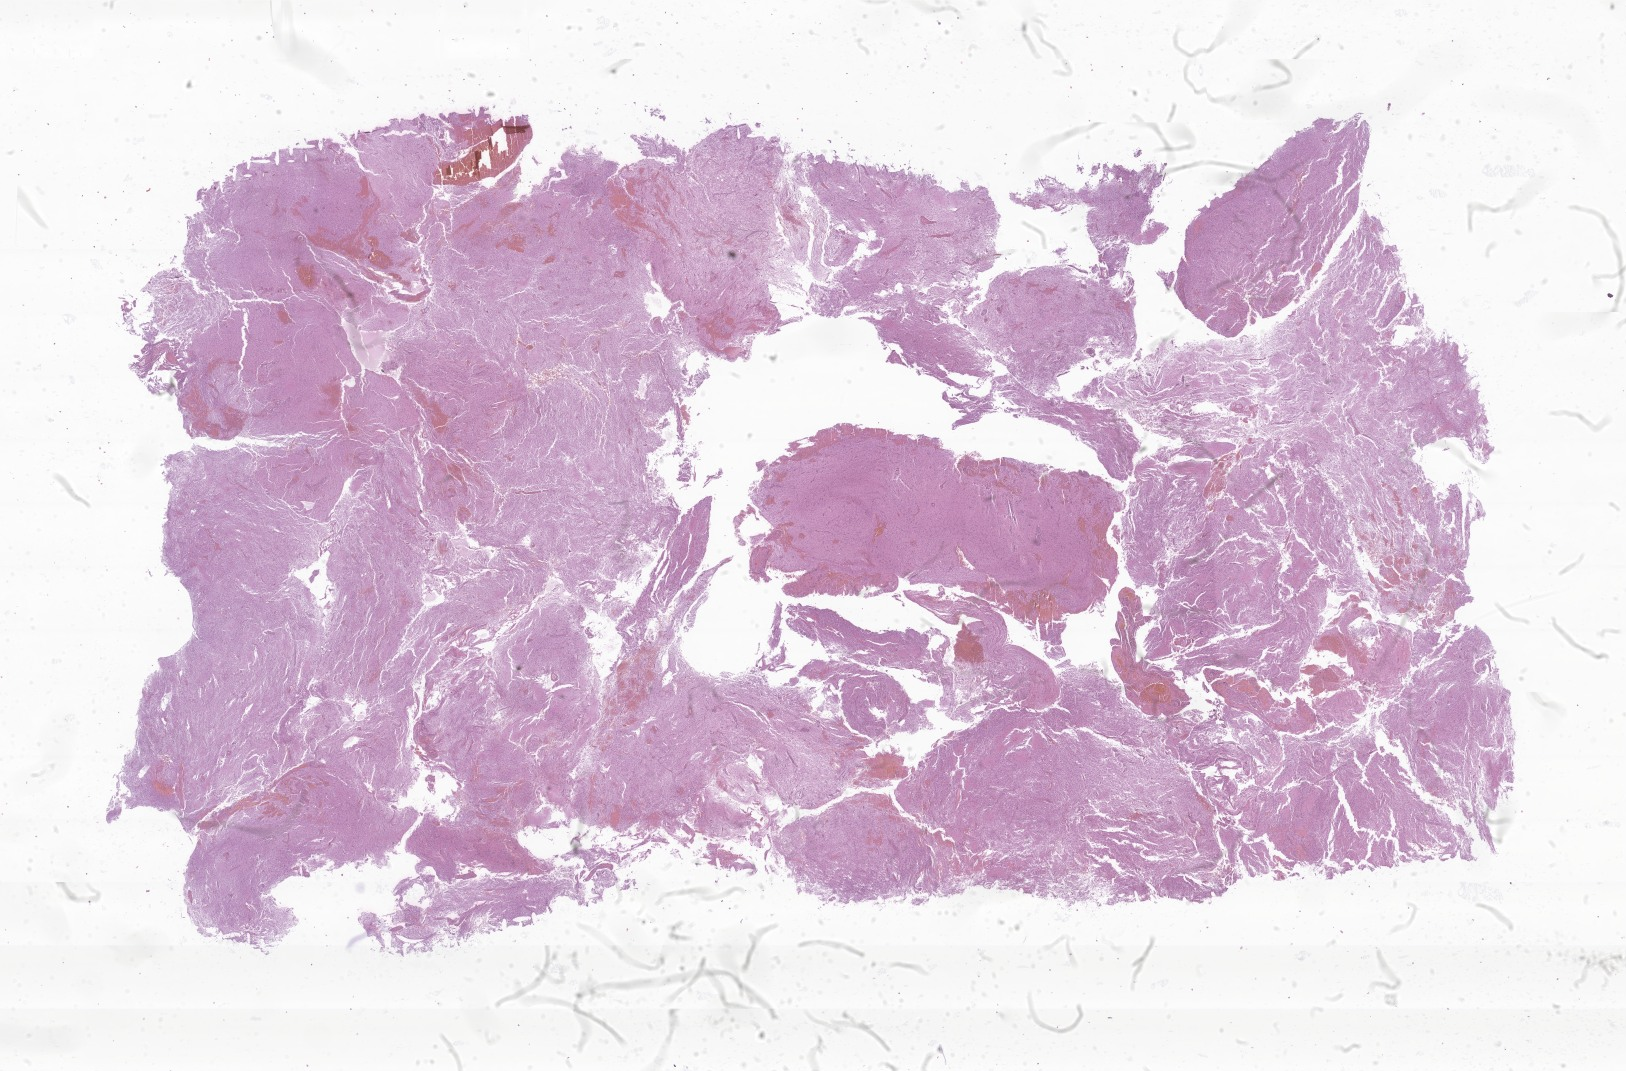
Digitized H&E-stained section of tumor tissue from the central nervous system — a low-resolution overview of the entire scanned area, about 27.4 x 18.1 mm, FFPE section. Female patient, age 118 months.
Diagnosis: Neoplasm, malignant.